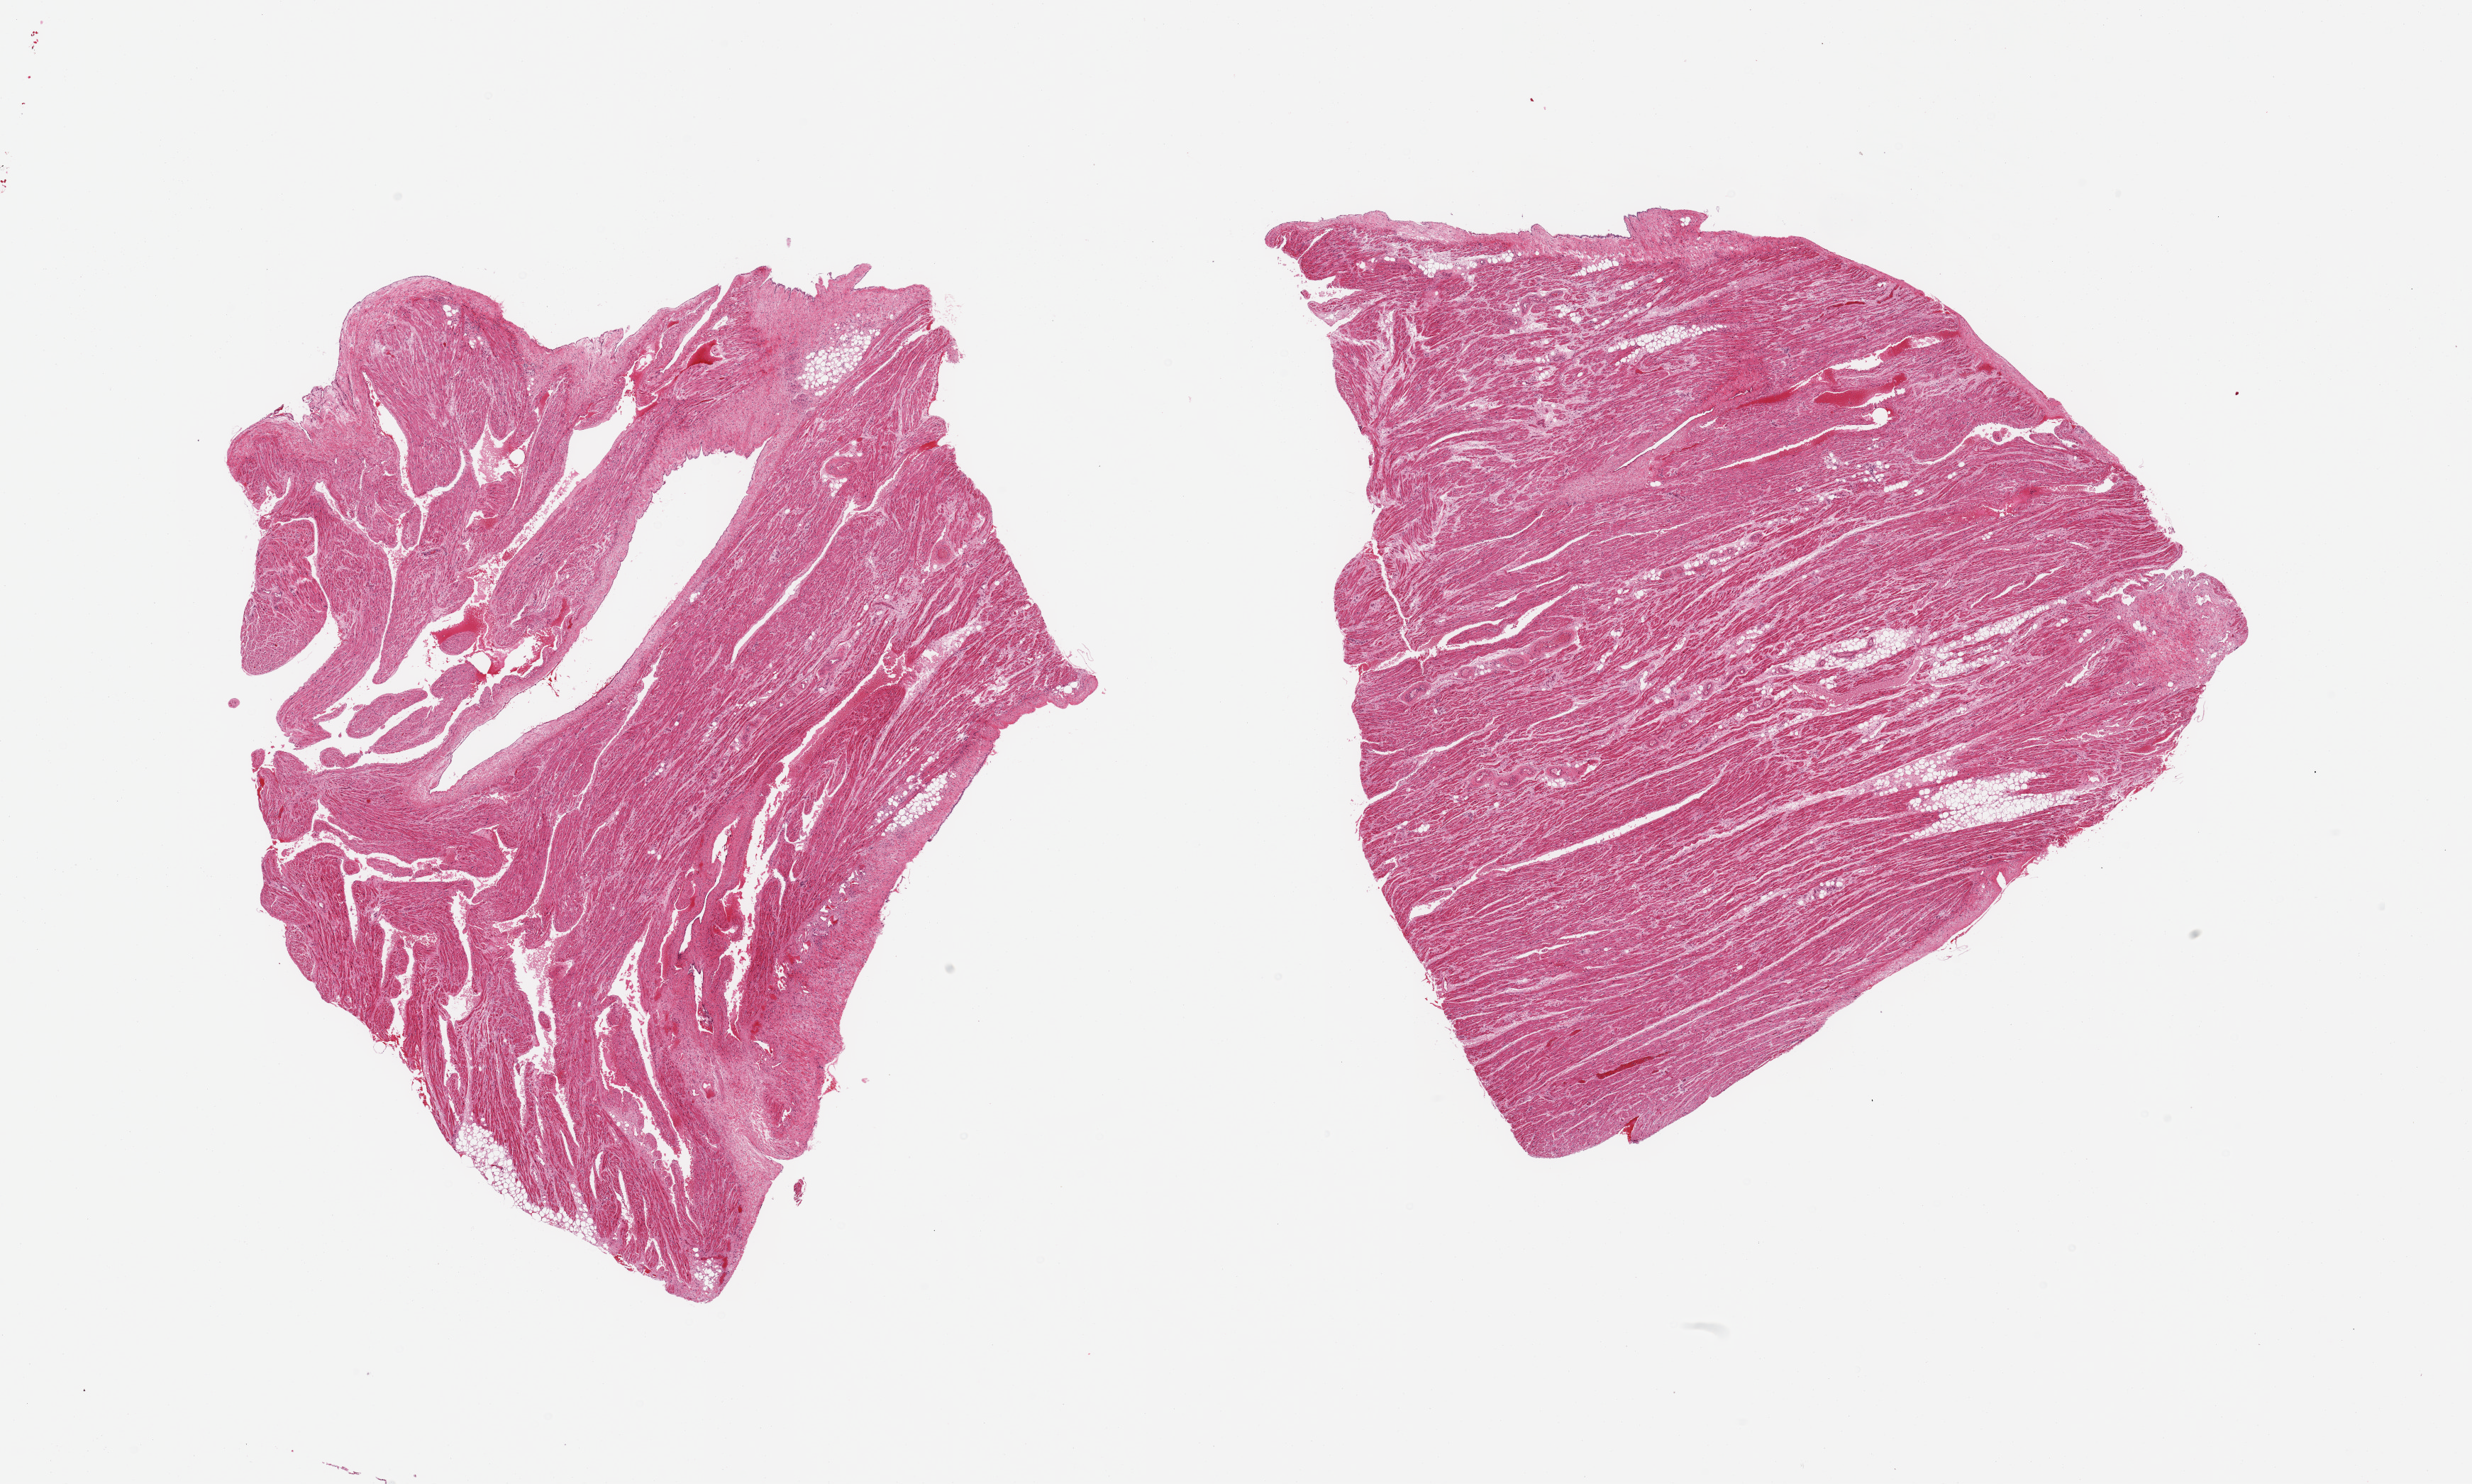
Digitized H&E-stained section — shown as a low-resolution overview of the whole scanned area (about 27.6 x 16.5 mm); PAXgene-fixed paraffin-embedded (PFPE) section; section of auricular appendage (target tissue); tissue donor sample. Donor sex: female.
Pathologist's review note for this sample: 2 pieces, no abnormalities.